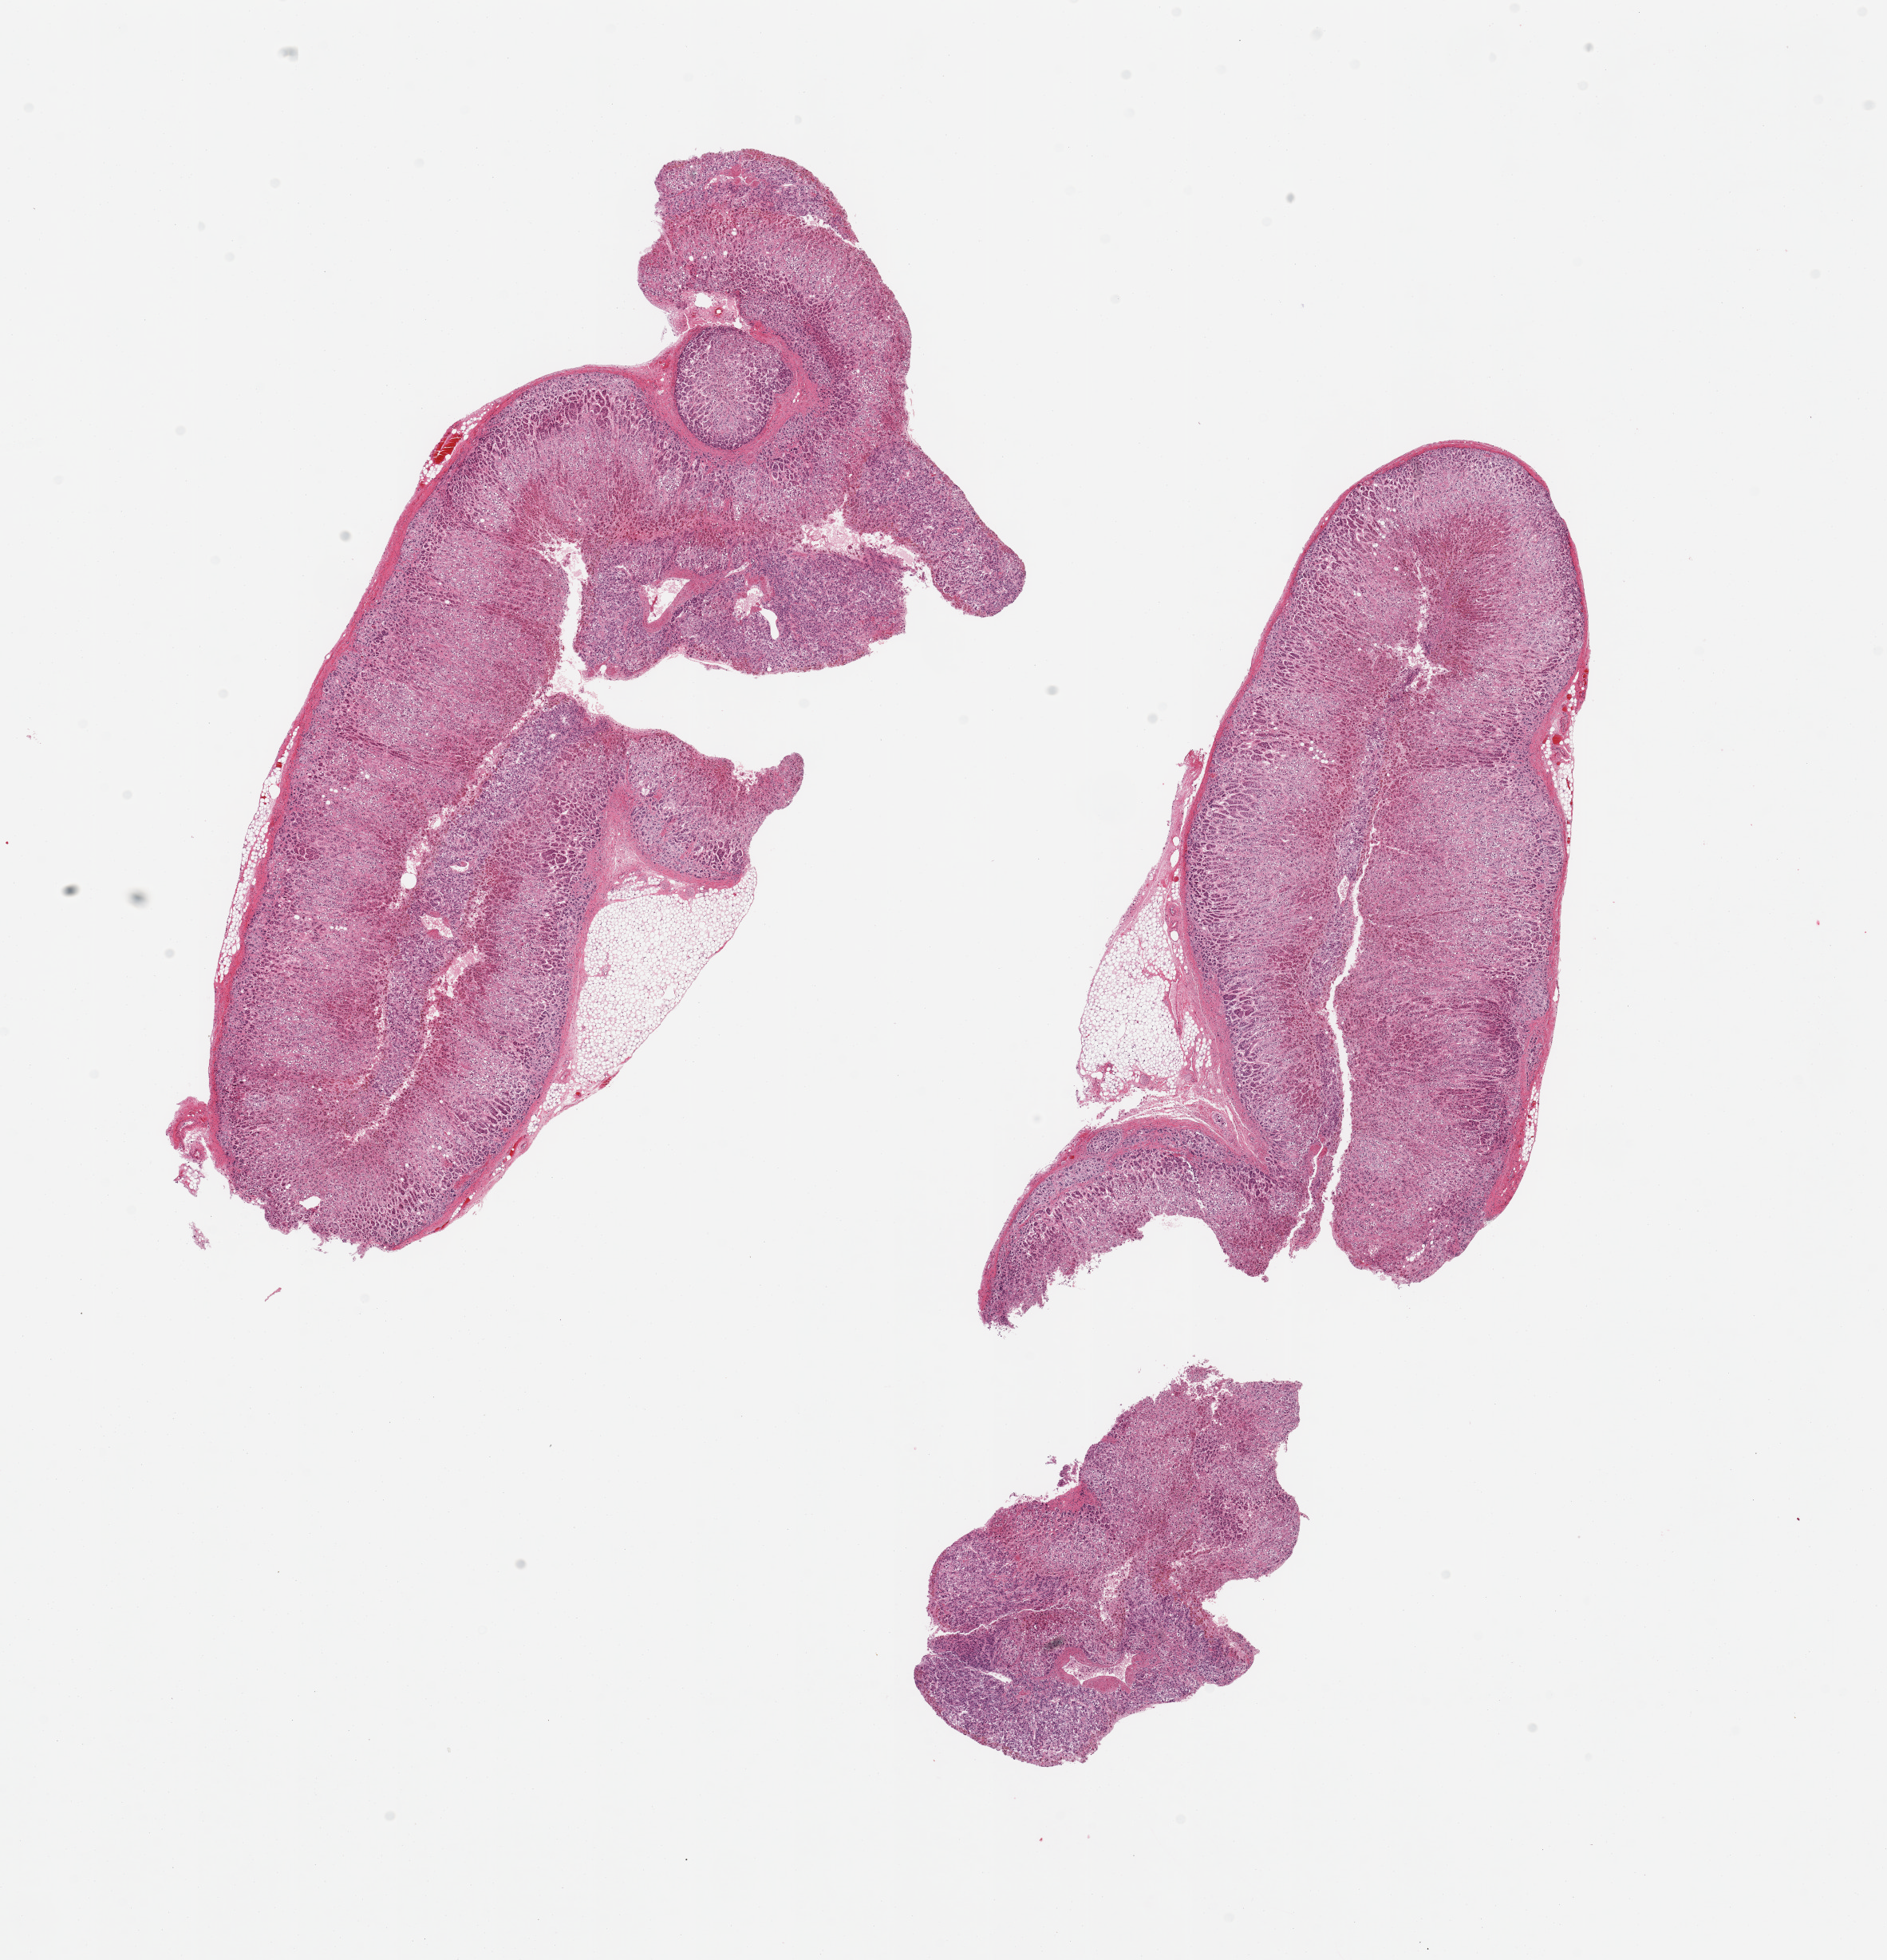
Whole-slide image, haematoxylin and eosin stain, shown as a low-resolution overview of the whole scanned area (about 18.7 x 19.4 mm, acquisition: 20x scan); PAXgene-fixed paraffin-embedded (PFPE) section; target tissue: adrenal gland; tissue donor sample. Donor: female.
Review note (as recorded): 2 pieces, cortex, trace adherent fat.